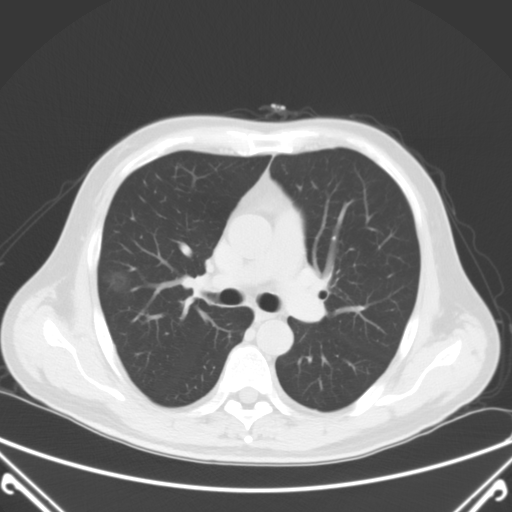
Chest CT, one axial slice. Position 46 of 72 along the scan axis. 120 kVp. Lung window (W 1500 / L -600 HU). 512 × 512 image matrix. Male patient, age 64 years. From the clinical record (not read from this slice): clinical TNM (as recorded): T1c N0 M0.
Outlined on this slice (bounding box drawn by a radiologist):
- lung tumour (recorded histology: adenocarcinoma): bounding box <104,266,128,293> (left, top, right, bottom; pixels)